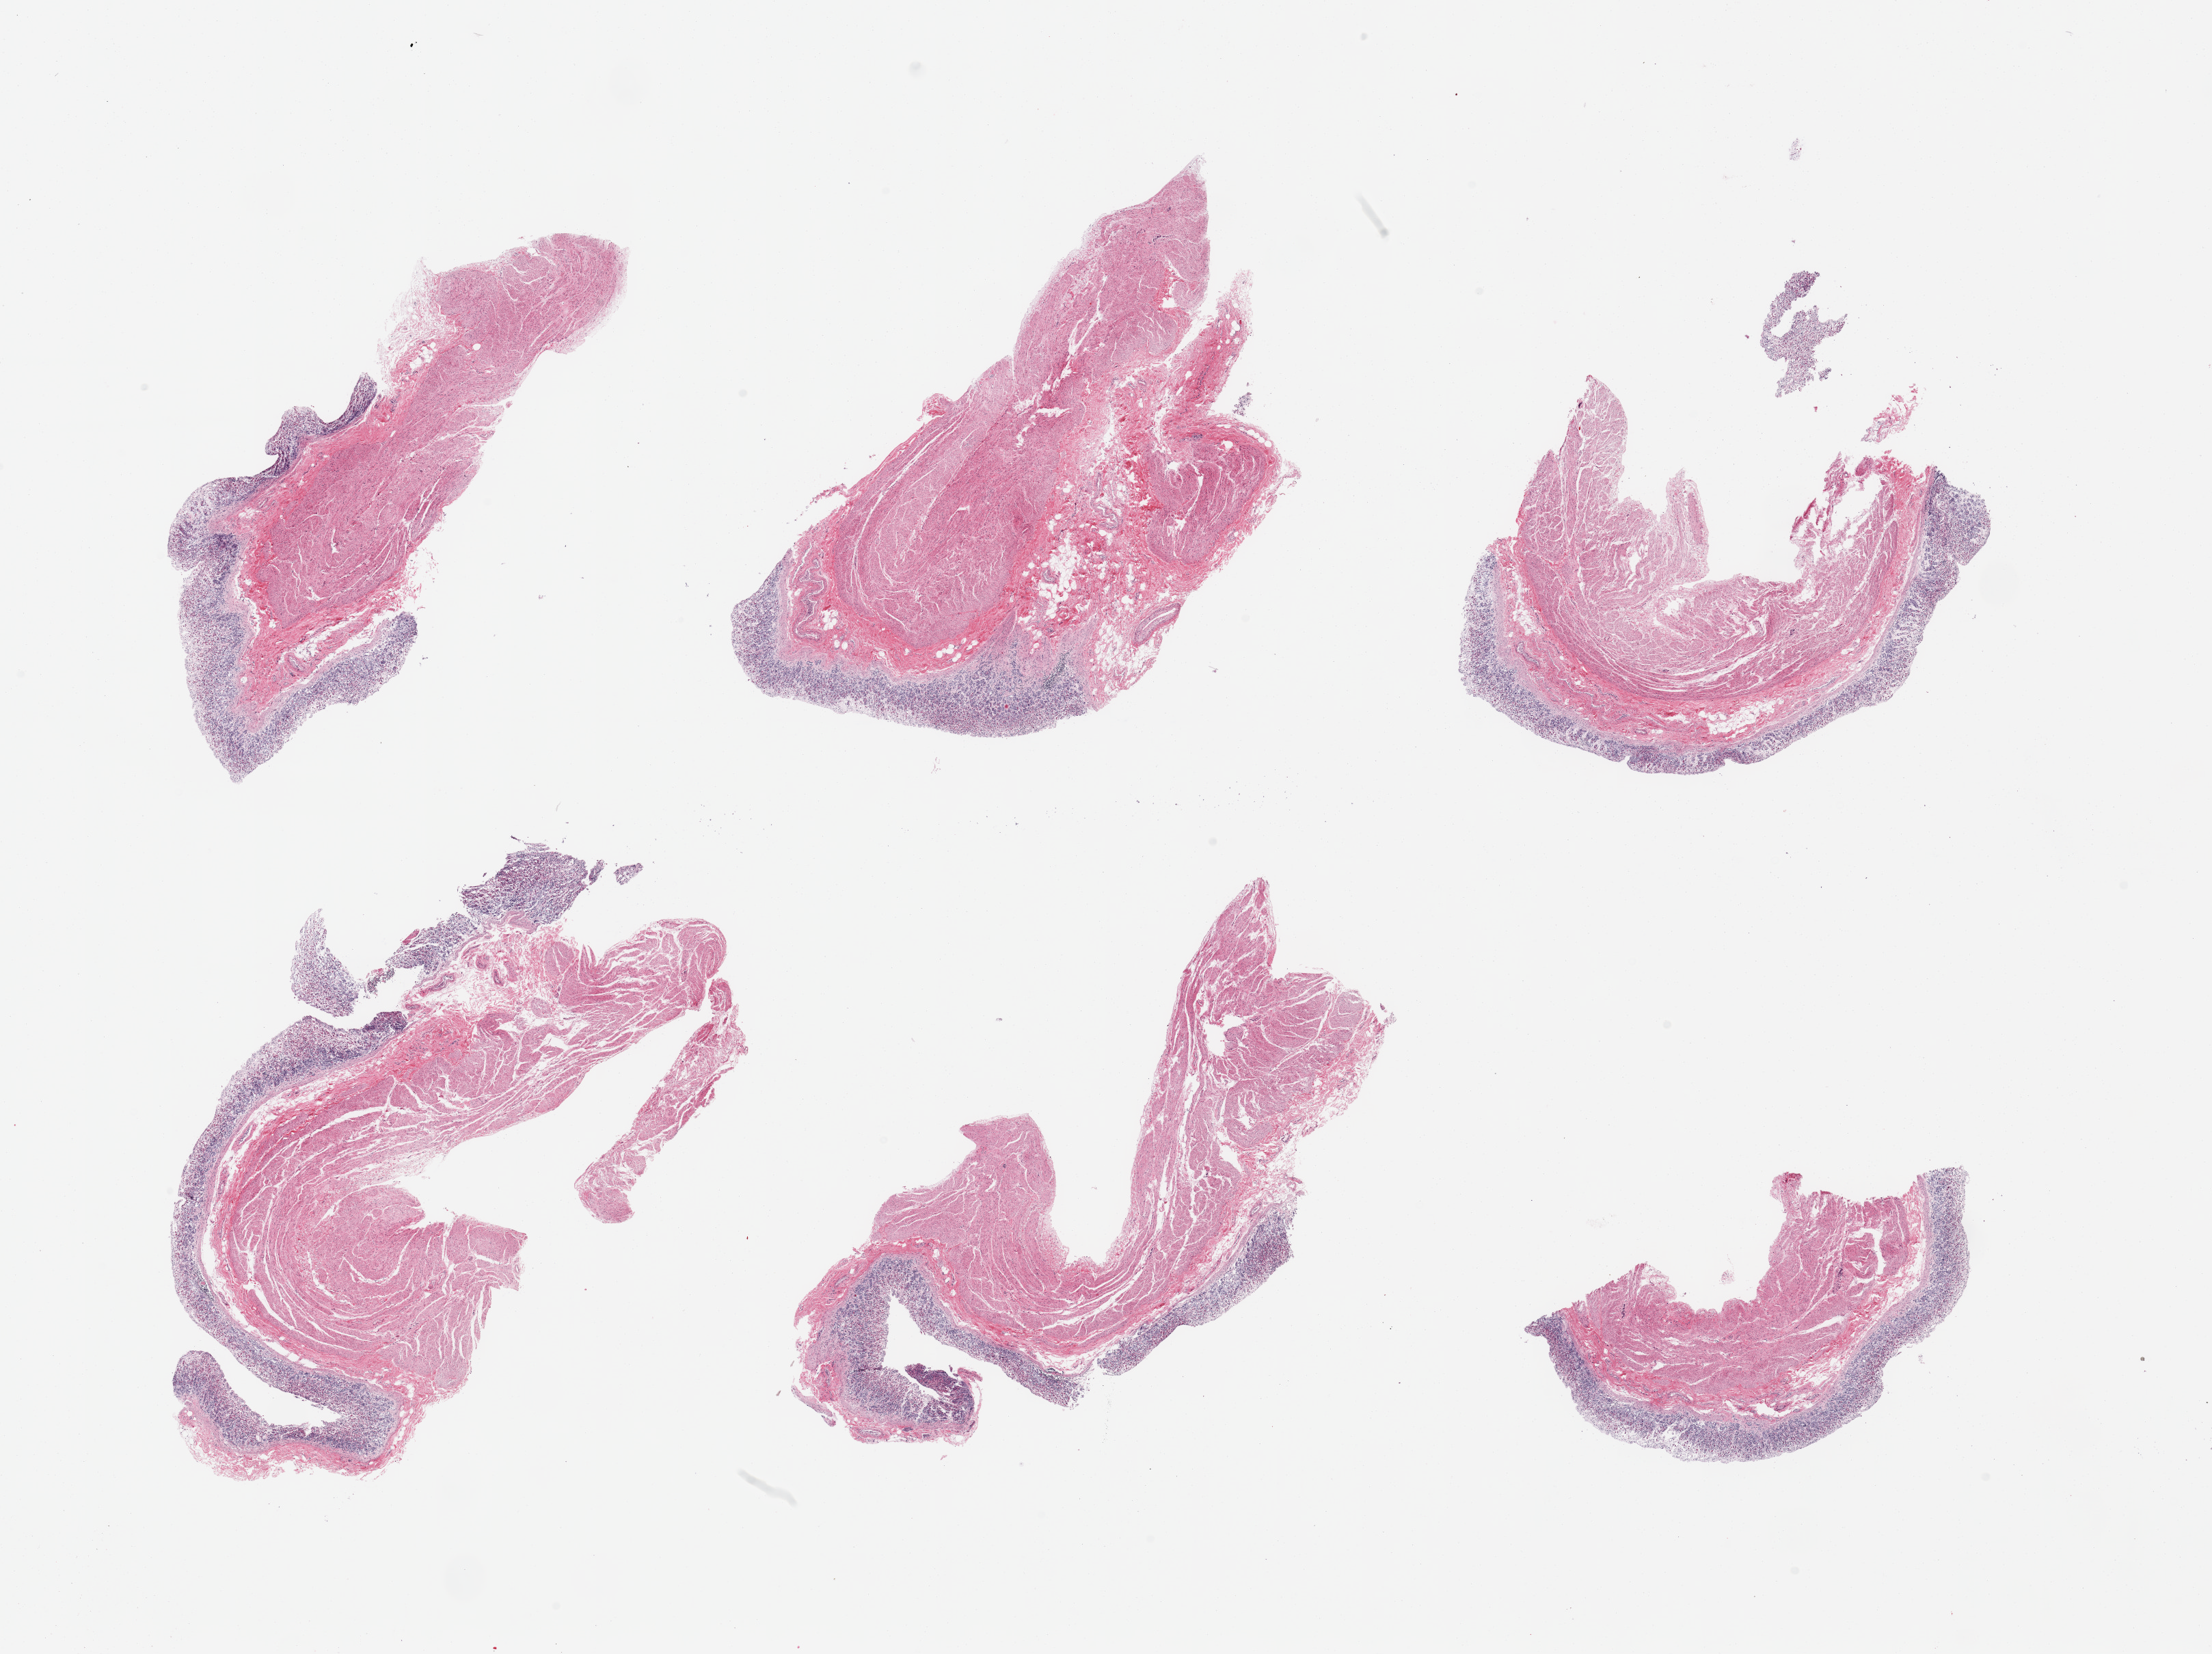
H&E whole-slide image, brightfield — whole scanned area (about 25.6 x 19.1 mm, from a 20x scan) shown as a low-resolution overview. PAXgene-fixed paraffin-embedded (PFPE) section. Section of stomach (target tissue). Tissue donor sample. Donor: female.
* pathologist's review note for this sample: 6 pieces, mucosa up to ~0.4mm but with advanced autolysis/sloughing